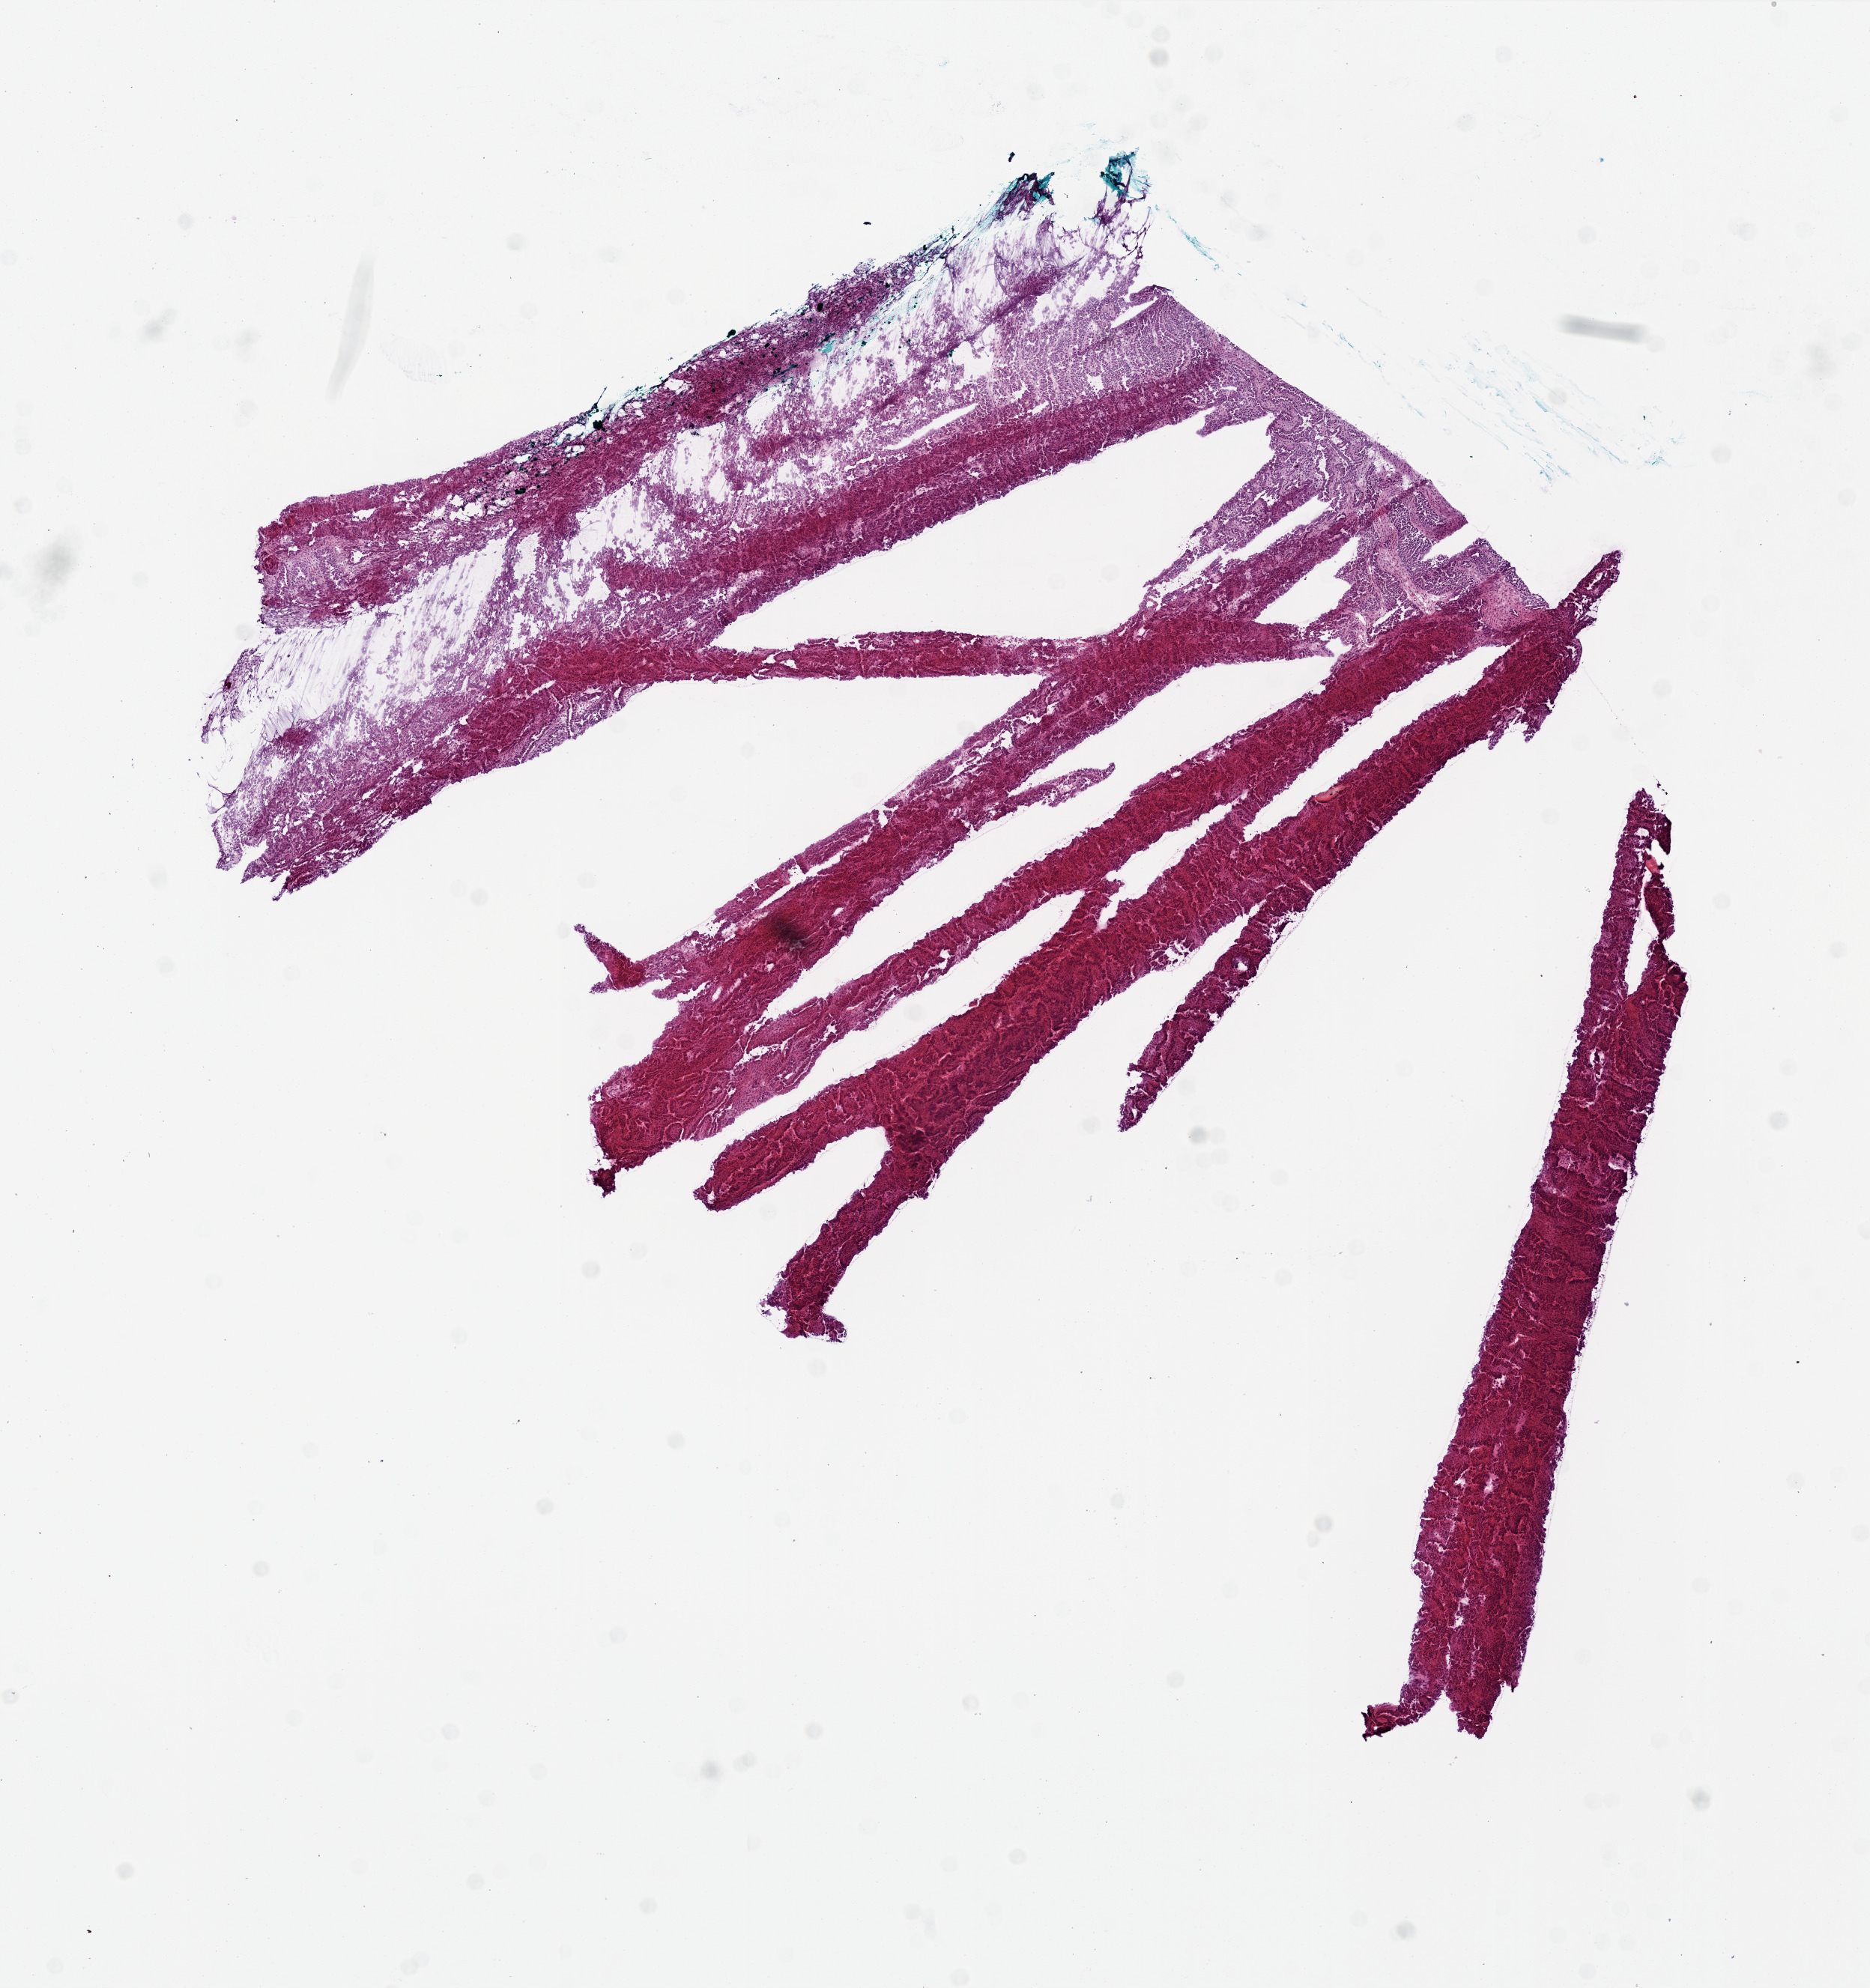
Digitized H&E tissue section (whole slide), whole scanned area (about 10.0 x 10.6 mm) shown as a low-resolution overview, frozen section, primary tumour sample from the ovary. Patient: female, age at initial diagnosis 80 years. Histologic grade: G3 (poorly differentiated). Slide review estimates, as recorded: tumour cells 90%, tumour nuclei 95%, normal cells 0%, stromal cells 10%, necrosis 0%.
* FIGO stage: IIC
* pathologic diagnosis: Serous cystadenocarcinoma, NOS